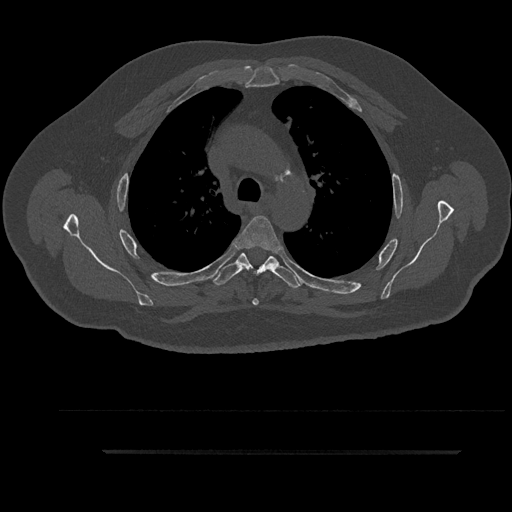
CT including the spine, one axial slice; slice 651 of 797 in the series (ordered by position); 120 kVp; bone window (W 1800 / L 400 HU); 0.5 mm slice thickness; 512 × 512 image matrix, field of view 432 × 432 mm. Patient: male, 63 years. From the clinical record (not read from this slice): primary cancer: renal.
Outlined on this slice (semi-automatic segmentation, software-assisted and operator-edited):
- T3 vertebra: box from (x=213, y=256) to (x=289, y=282) px
- T4 vertebra: (x=235, y=216)–(x=281, y=306)
- T5 vertebra: (x=214, y=253)–(x=300, y=289)